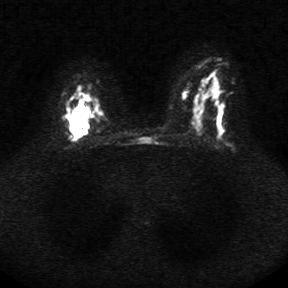
Breast MRI, one axial slice. Slice 21 of 34 in the series (ordered by position). Diffusion-weighted series; image 2 of 4 stored at this slice position (different b-values; order by instance number). 1.5 T. 288 × 288 image matrix, field of view 340 × 340 mm. Female patient.
Structures marked on this image (expert manual segmentation):
- tumour on diffusion-weighted imaging: bounding box (x1, y1, x2, y2) in pixels: (68, 108, 85, 132)